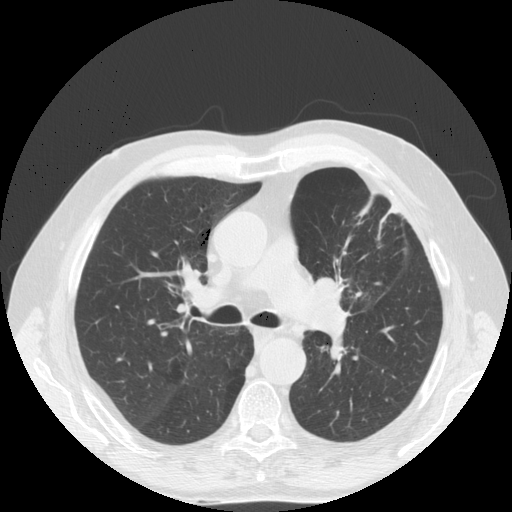
Low-dose screening chest CT, one axial slice; position 110 of 170 along the scan axis; reconstruction kernel STANDARD; 140 kVp; lung window (W 1500 / L -600 HU); 2.5 mm slice thickness; 512 × 512 image matrix, field of view 380 × 380 mm.
Outlined on this slice (manually delineated by an expert):
- lesion 1 (tumor, upper lobe of left lung): box from (x=314, y=275) to (x=335, y=297) px